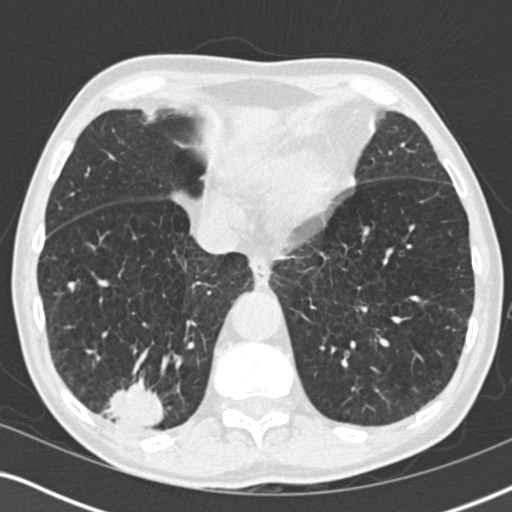
Low-dose screening chest CT, one axial slice. Slice 59 of 196 in the series (ordered by position). Reconstruction kernel B30f. Lung window (W 1500 / L -600 HU). 2 mm slice thickness. 512 × 512 image matrix, field of view 330 × 330 mm.
Structures marked on this image (outlined manually by an expert reader):
- lesion 3 (tumor, lower lobe of right lung): bounding box <107,381,164,428> (left, top, right, bottom; pixels)